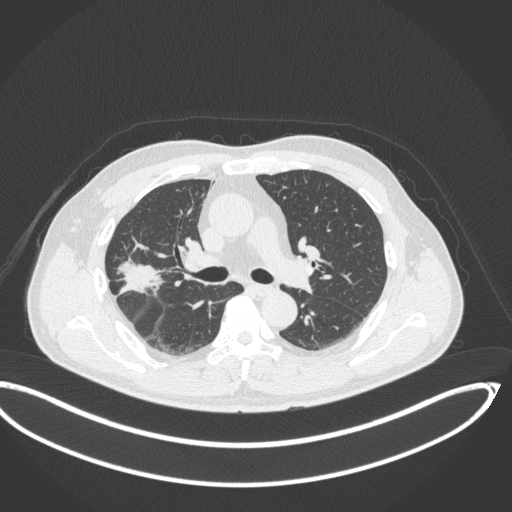
Chest CT, one axial slice; slice 209 of 341 in the series (ordered by position); lung window (W 1500 / L -600 HU); 512 × 512 image matrix. Patient: male, 63 years. Case-level facts recorded for this patient, not image findings: clinical TNM (as recorded): T1c N0 M0.
Outlined on this slice (rectangle marked by the reading radiologist):
- lung tumour (recorded histology: adenocarcinoma): bounding box <115,252,166,301> (left, top, right, bottom; pixels)